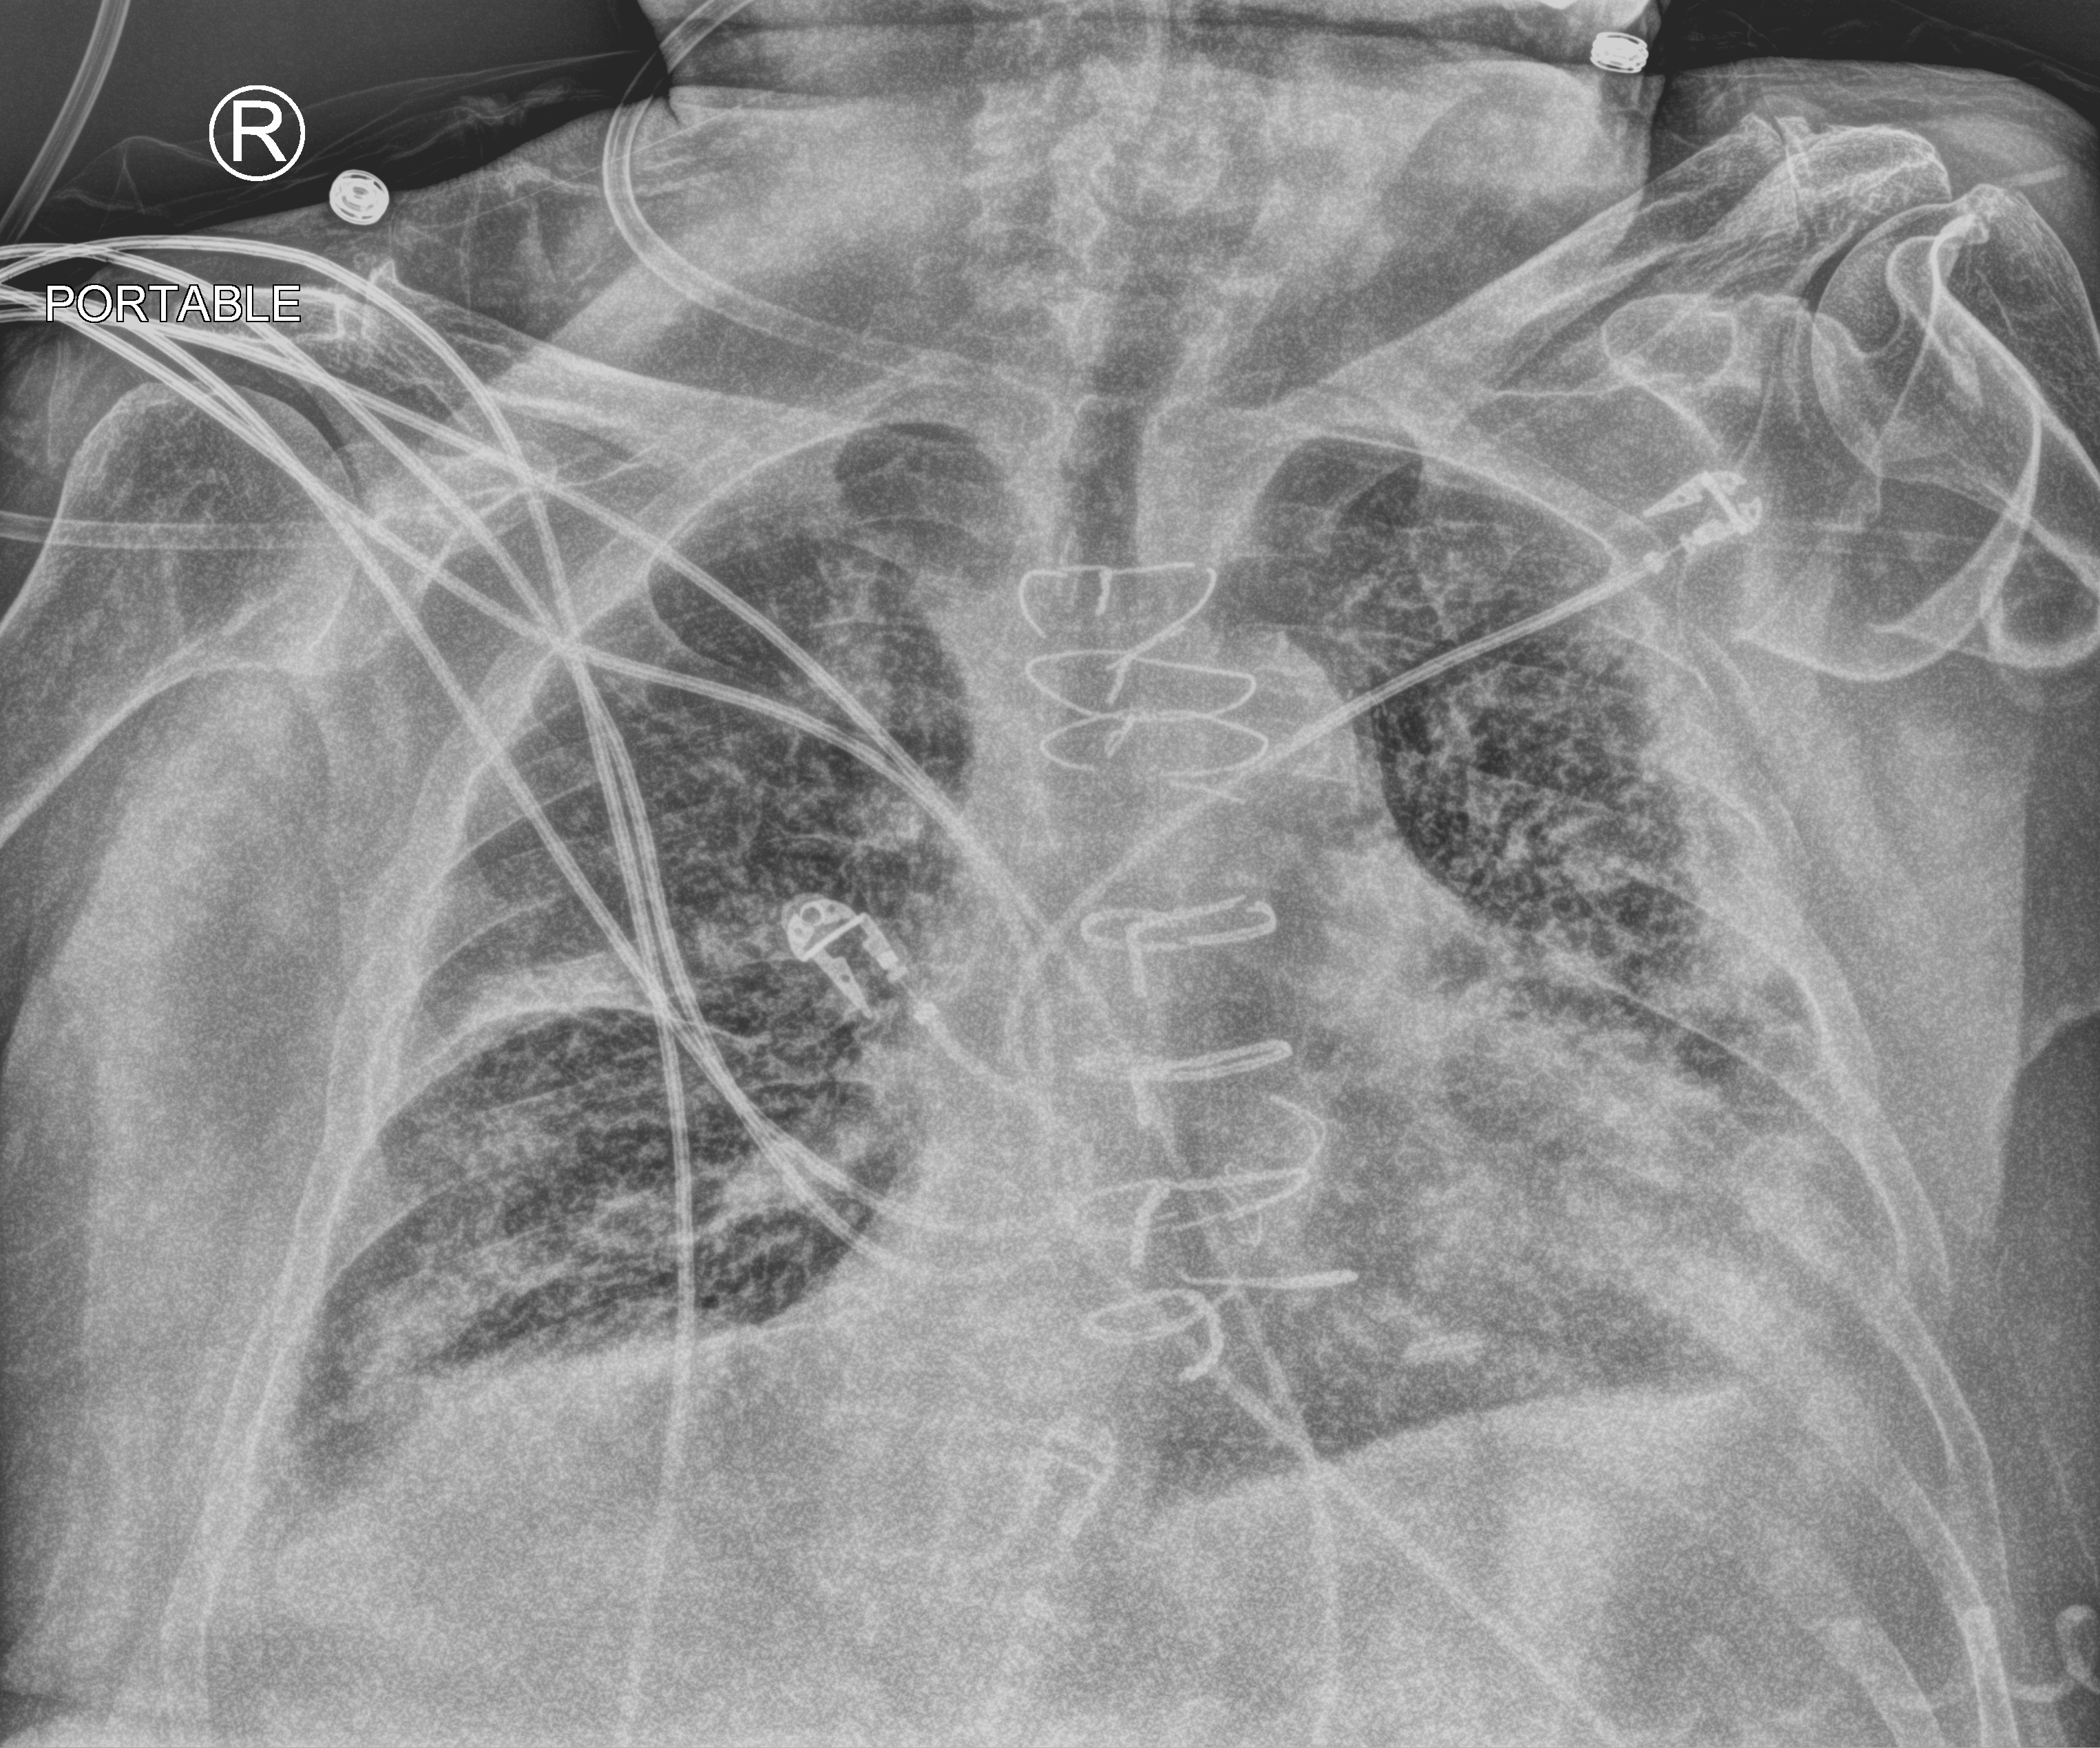
Bedside chest radiograph (computed radiography). Patient hospitalised with COVID-19; male, aged 75–90 years.
Admission-level facts for this patient (not findings on this image; timing relative to this image not recorded): admitted to intensive care during this hospital stay: no; mechanically ventilated during this hospital stay: no.